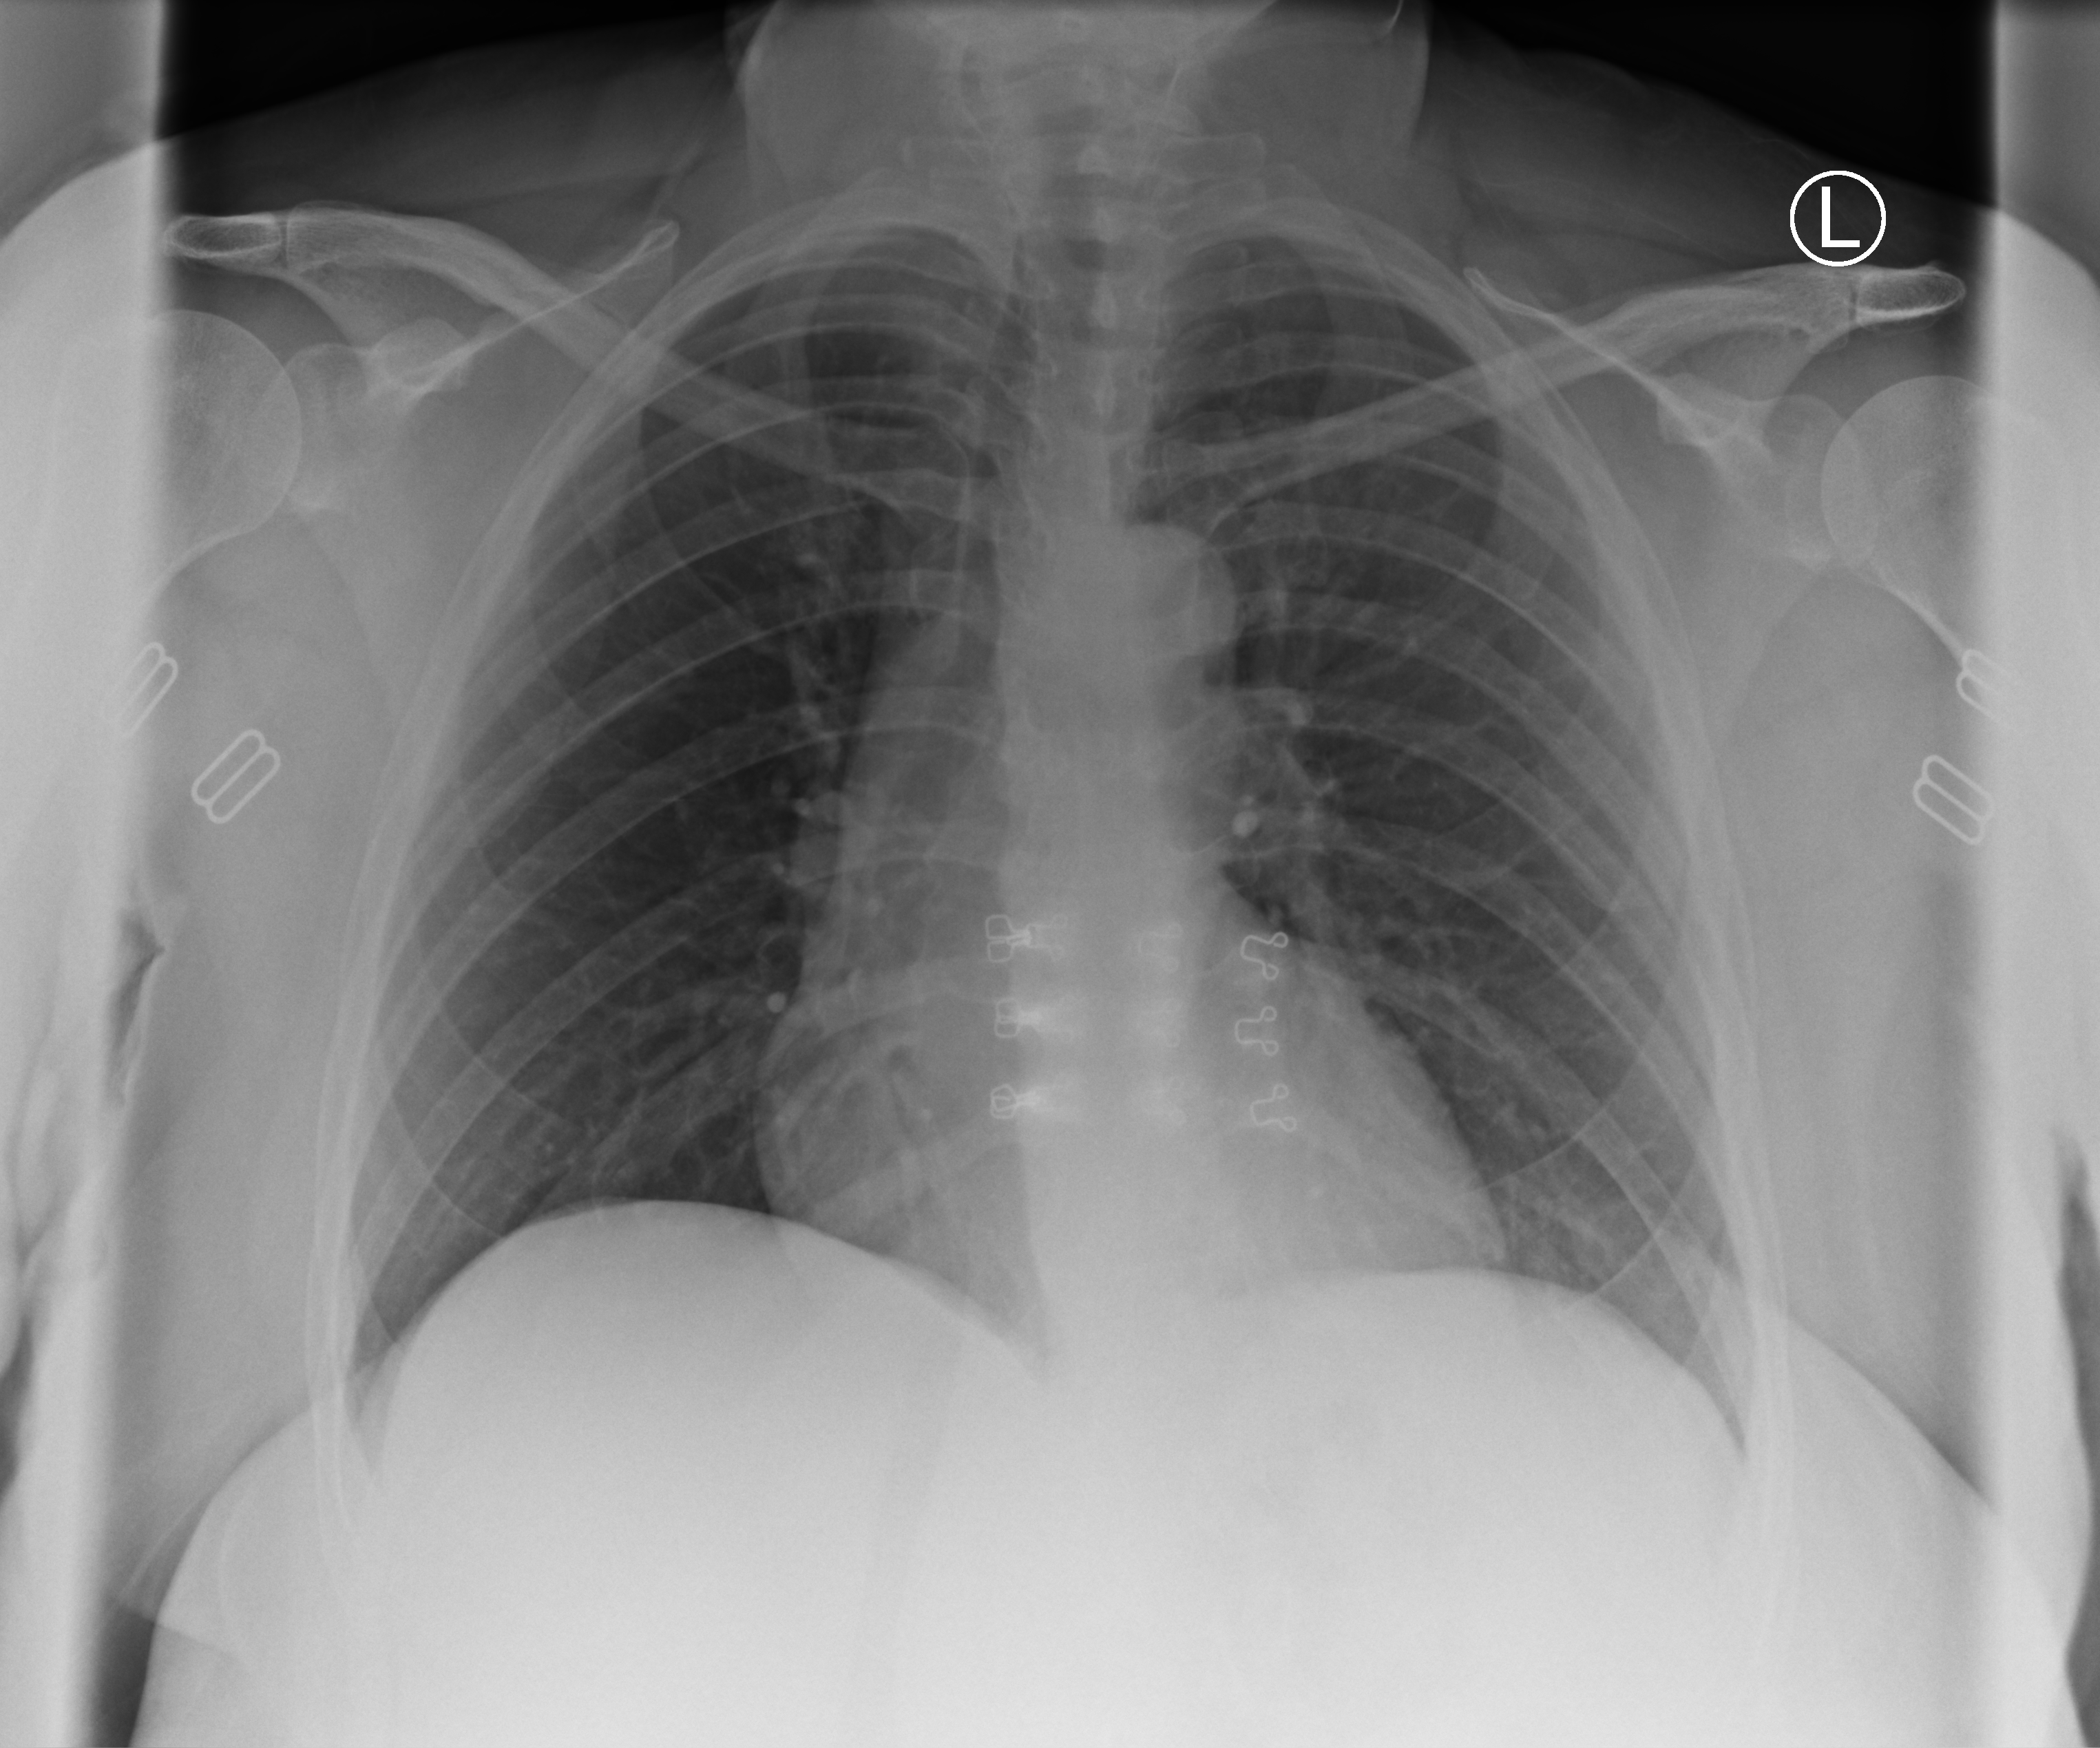
Chest X-ray (portable); anteroposterior (AP) projection. Patient hospitalised with COVID-19; female, aged 18–59 years.
From the hospital-stay record, not from the radiograph (when in the stay this image was taken is not recorded):
- mechanically ventilated during this hospital stay: no
- length of hospital stay: 1 day
- admitted to intensive care during this hospital stay: no